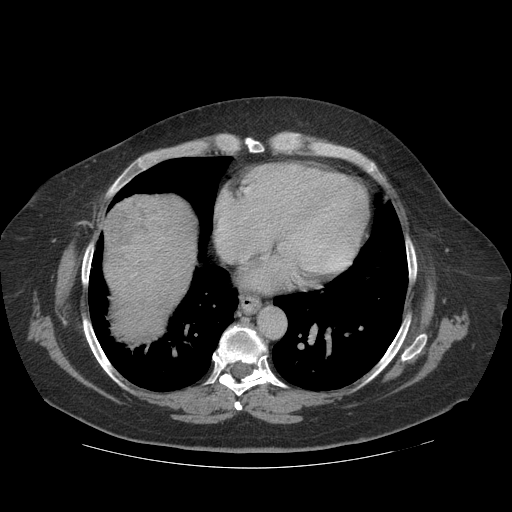
Contrast-enhanced abdominal CT (liver protocol), one axial slice. Position 107 of 121 along the scan axis. Reconstruction kernel STANDARD. Soft-tissue window (W 400 / L 40 HU). 512 × 512 image matrix. From the clinical record (not read from this slice): diagnosis: hepatocellular carcinoma (patient treated with transarterial chemoembolisation; whether this scan precedes or follows treatment is not stated here); TNM stage (as recorded): Stage-IIIA; Child-Pugh class: A; tumour differentiation: well differentiated; tumour size: 7.4 cm.
Annotated regions visible in this slice (semi-automatically segmented with operator editing):
- liver parenchyma outside the tumour (the mass and vessels are separate outlines, so this box may not span the whole liver): bounding box [x1, y1, x2, y2] px = [104, 194, 196, 336]
- mass: [102, 205, 145, 245]